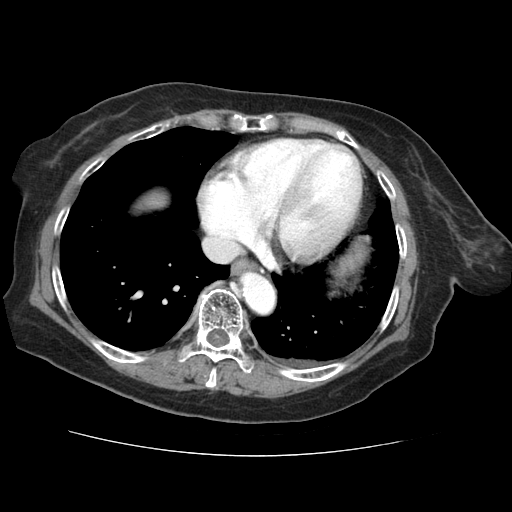
Contrast-enhanced abdominal CT (liver protocol), one axial slice; slice 63 of 73 in the series (ordered by position); reconstruction kernel STANDARD; soft-tissue window (W 400 / L 40 HU); 2.5 mm slice thickness; 512 × 512 image matrix, field of view 360 × 360 mm. Case-level facts recorded for this patient, not image findings: diagnosis: hepatocellular carcinoma (patient treated with transarterial chemoembolisation; whether this scan precedes or follows treatment is not stated here); TNM stage (as recorded): Stage-IVB; Child-Pugh class: A; tumour nodularity: uninodular.
Annotated regions visible in this slice (semi-automatic segmentation, software-assisted and operator-edited):
- liver parenchyma outside the tumour (the mass and vessels are separate outlines, so this box may not span the whole liver): bounding box (x1, y1, x2, y2) in pixels: (142, 192, 166, 208)